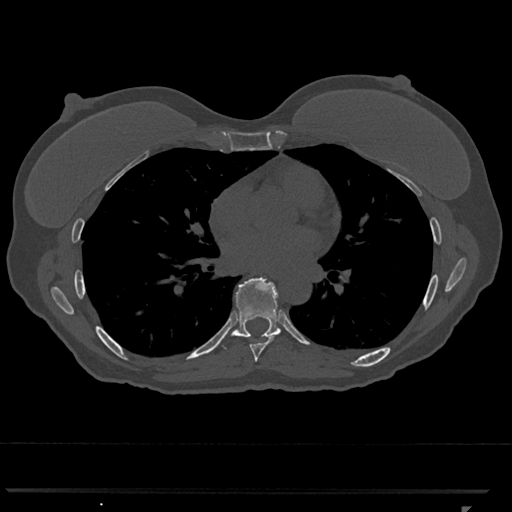
CT including the spine, one axial slice. Position 687 of 793 along the scan axis. Reconstruction kernel Br40s/3. Bone window (W 1800 / L 400 HU). 512 × 512 image matrix, field of view 380 × 380 mm. Female patient, age 62 years. Case-level facts recorded for this patient, not image findings: primary cancer: renal.
Outlined on this slice (semi-automatic segmentation, software-assisted and operator-edited):
- T7 vertebra: bounding box (x1, y1, x2, y2) in pixels: (243, 335, 276, 362)
- T8 vertebra: (219, 277, 281, 349)